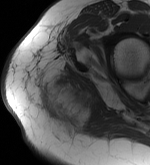
MRI of an extremity soft-tissue mass, one axial slice. Slice 41 of 56 in the series (ordered by position). MR volume resampled by the dataset authors to the PET/CT grid (not the native acquisition matrix). 150 × 165 image matrix, field of view 146 × 161 mm. Female patient. From the clinical record (not read from this slice): histological type: epithelioid sarcoma with vascular differentiation; site of the primary tumour: right buttock.
Outlined on this slice (expert contour drawn on MRI and transferred to this co-registered scan by the dataset authors):
- gross tumour volume (mass): bounding box <37,77,93,128> (left, top, right, bottom; pixels)